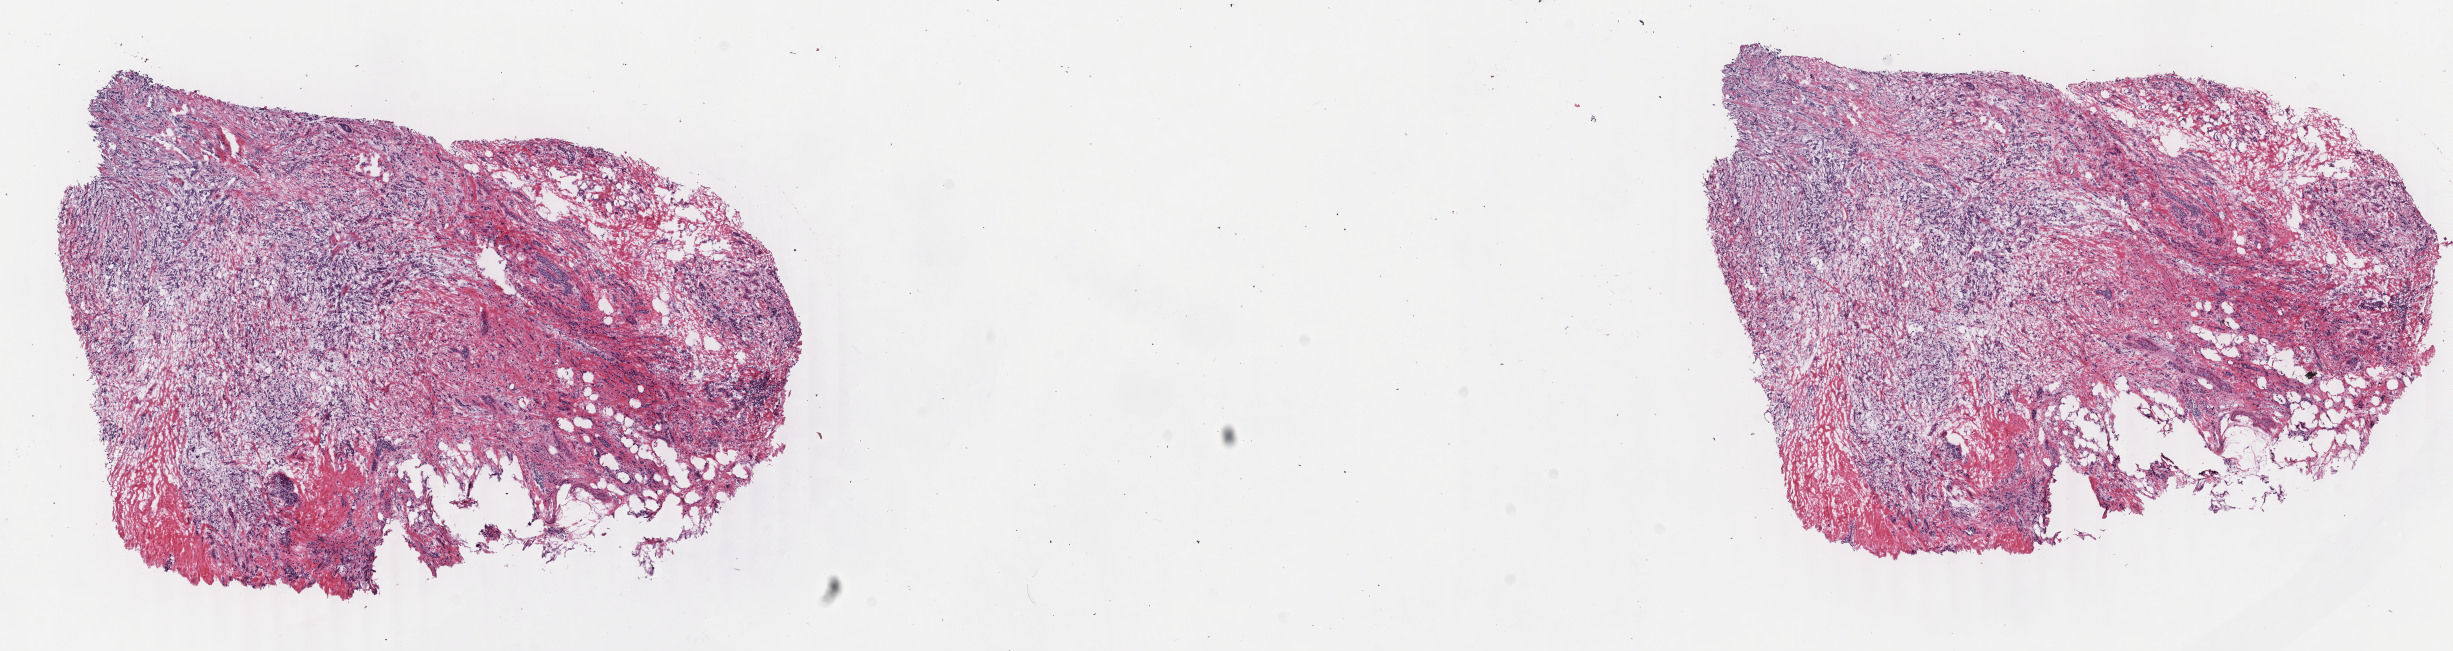
H&E whole-slide image — whole scanned area (about 19.5 x 5.2 mm, from a 40x scan) shown as a low-resolution overview; frozen section from the top of the tissue portion; sample: primary tumour, breast. Patient: female, age at initial diagnosis 43 years. Pathologist review of this section (percent, as recorded): tumour cells 80%, tumour nuclei 80%, normal cells 3%, stromal cells 17%, necrosis 0%. Infiltration values recorded for this section: lymphocyte infiltration 2%, monocyte infiltration 1%, neutrophil infiltration 1%.
* AJCC pathologic stage: IIIA
* lymph nodes positive (case pathology): 7 of 19 examined
* pathologic diagnosis: Infiltrating duct and lobular carcinoma
* laterality: left